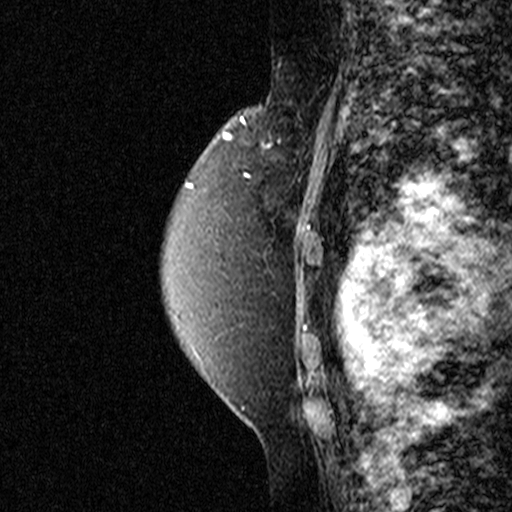
Breast MRI (dynamic contrast-enhanced), one sagittal slice; slice 32 of 44 in the series (ordered by position); dynamic contrast-enhanced study with each time point stored as its own series, time point 2 of 3 at this slice position (early post-contrast, ordered by acquisition time); 1.5 T; TE 4.5 ms, TR 11 ms; 512 × 512 image matrix. Patient: female, 49 years. Case-level facts recorded for this patient, not image findings: setting: breast cancer imaged before/during neoadjuvant chemotherapy; receptor status: triple-negative.
Outlined on this slice (semi-automatic segmentation, software-assisted and operator-edited):
- analysis volume of interest (the breast-tissue region the enhancement analysis was run in; not a lesion): bounding box [x1, y1, x2, y2] px = [252, 100, 335, 197]
- tumour enhancement mask (voxels above the 90 % enhancement threshold inside the analysis volume of interest): [264, 139, 281, 148]